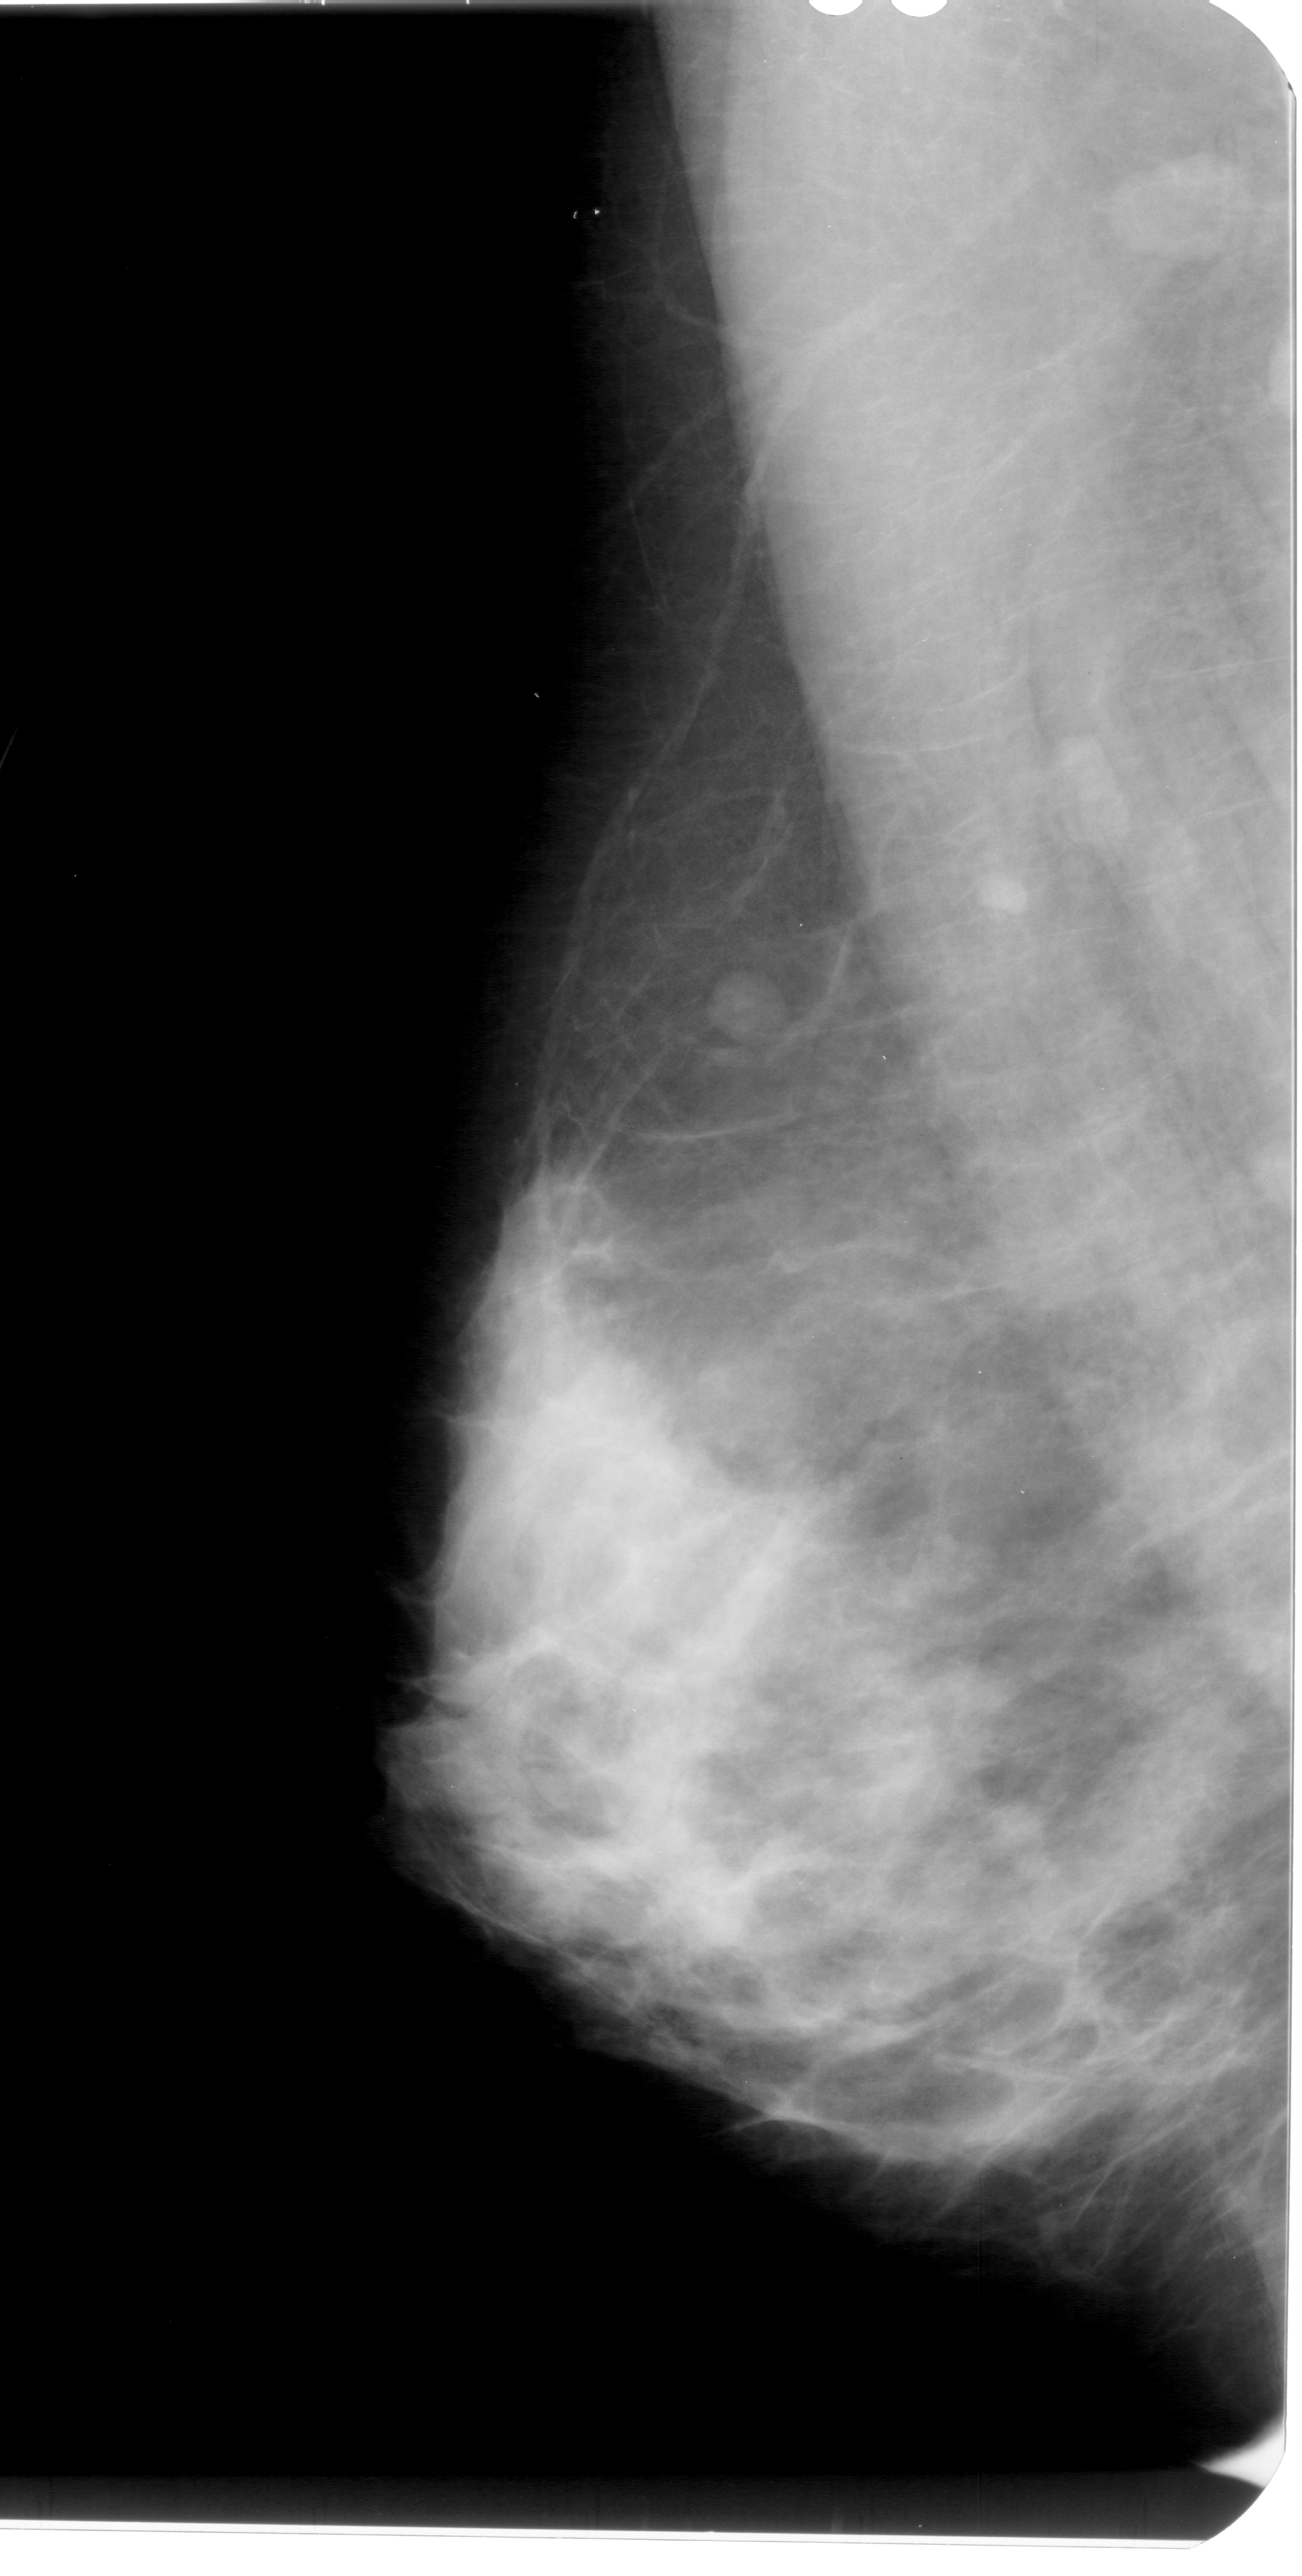
Scanned film-screen mammogram. Left breast. MLO view. BI-RADS breast density category 4 (scale 1–4). 1302 × 2576 image matrix.
Expert-marked regions of interest on this image (one box per marked abnormality):
- calcifications, morphology amorphous, distribution clustered; BI-RADS assessment category 4; subtlety rating 2 on a 1 (subtle) to 5 (obvious) scale; pathology result (as recorded, not read from the image): benign: box from (x=681, y=1814) to (x=856, y=1977) px